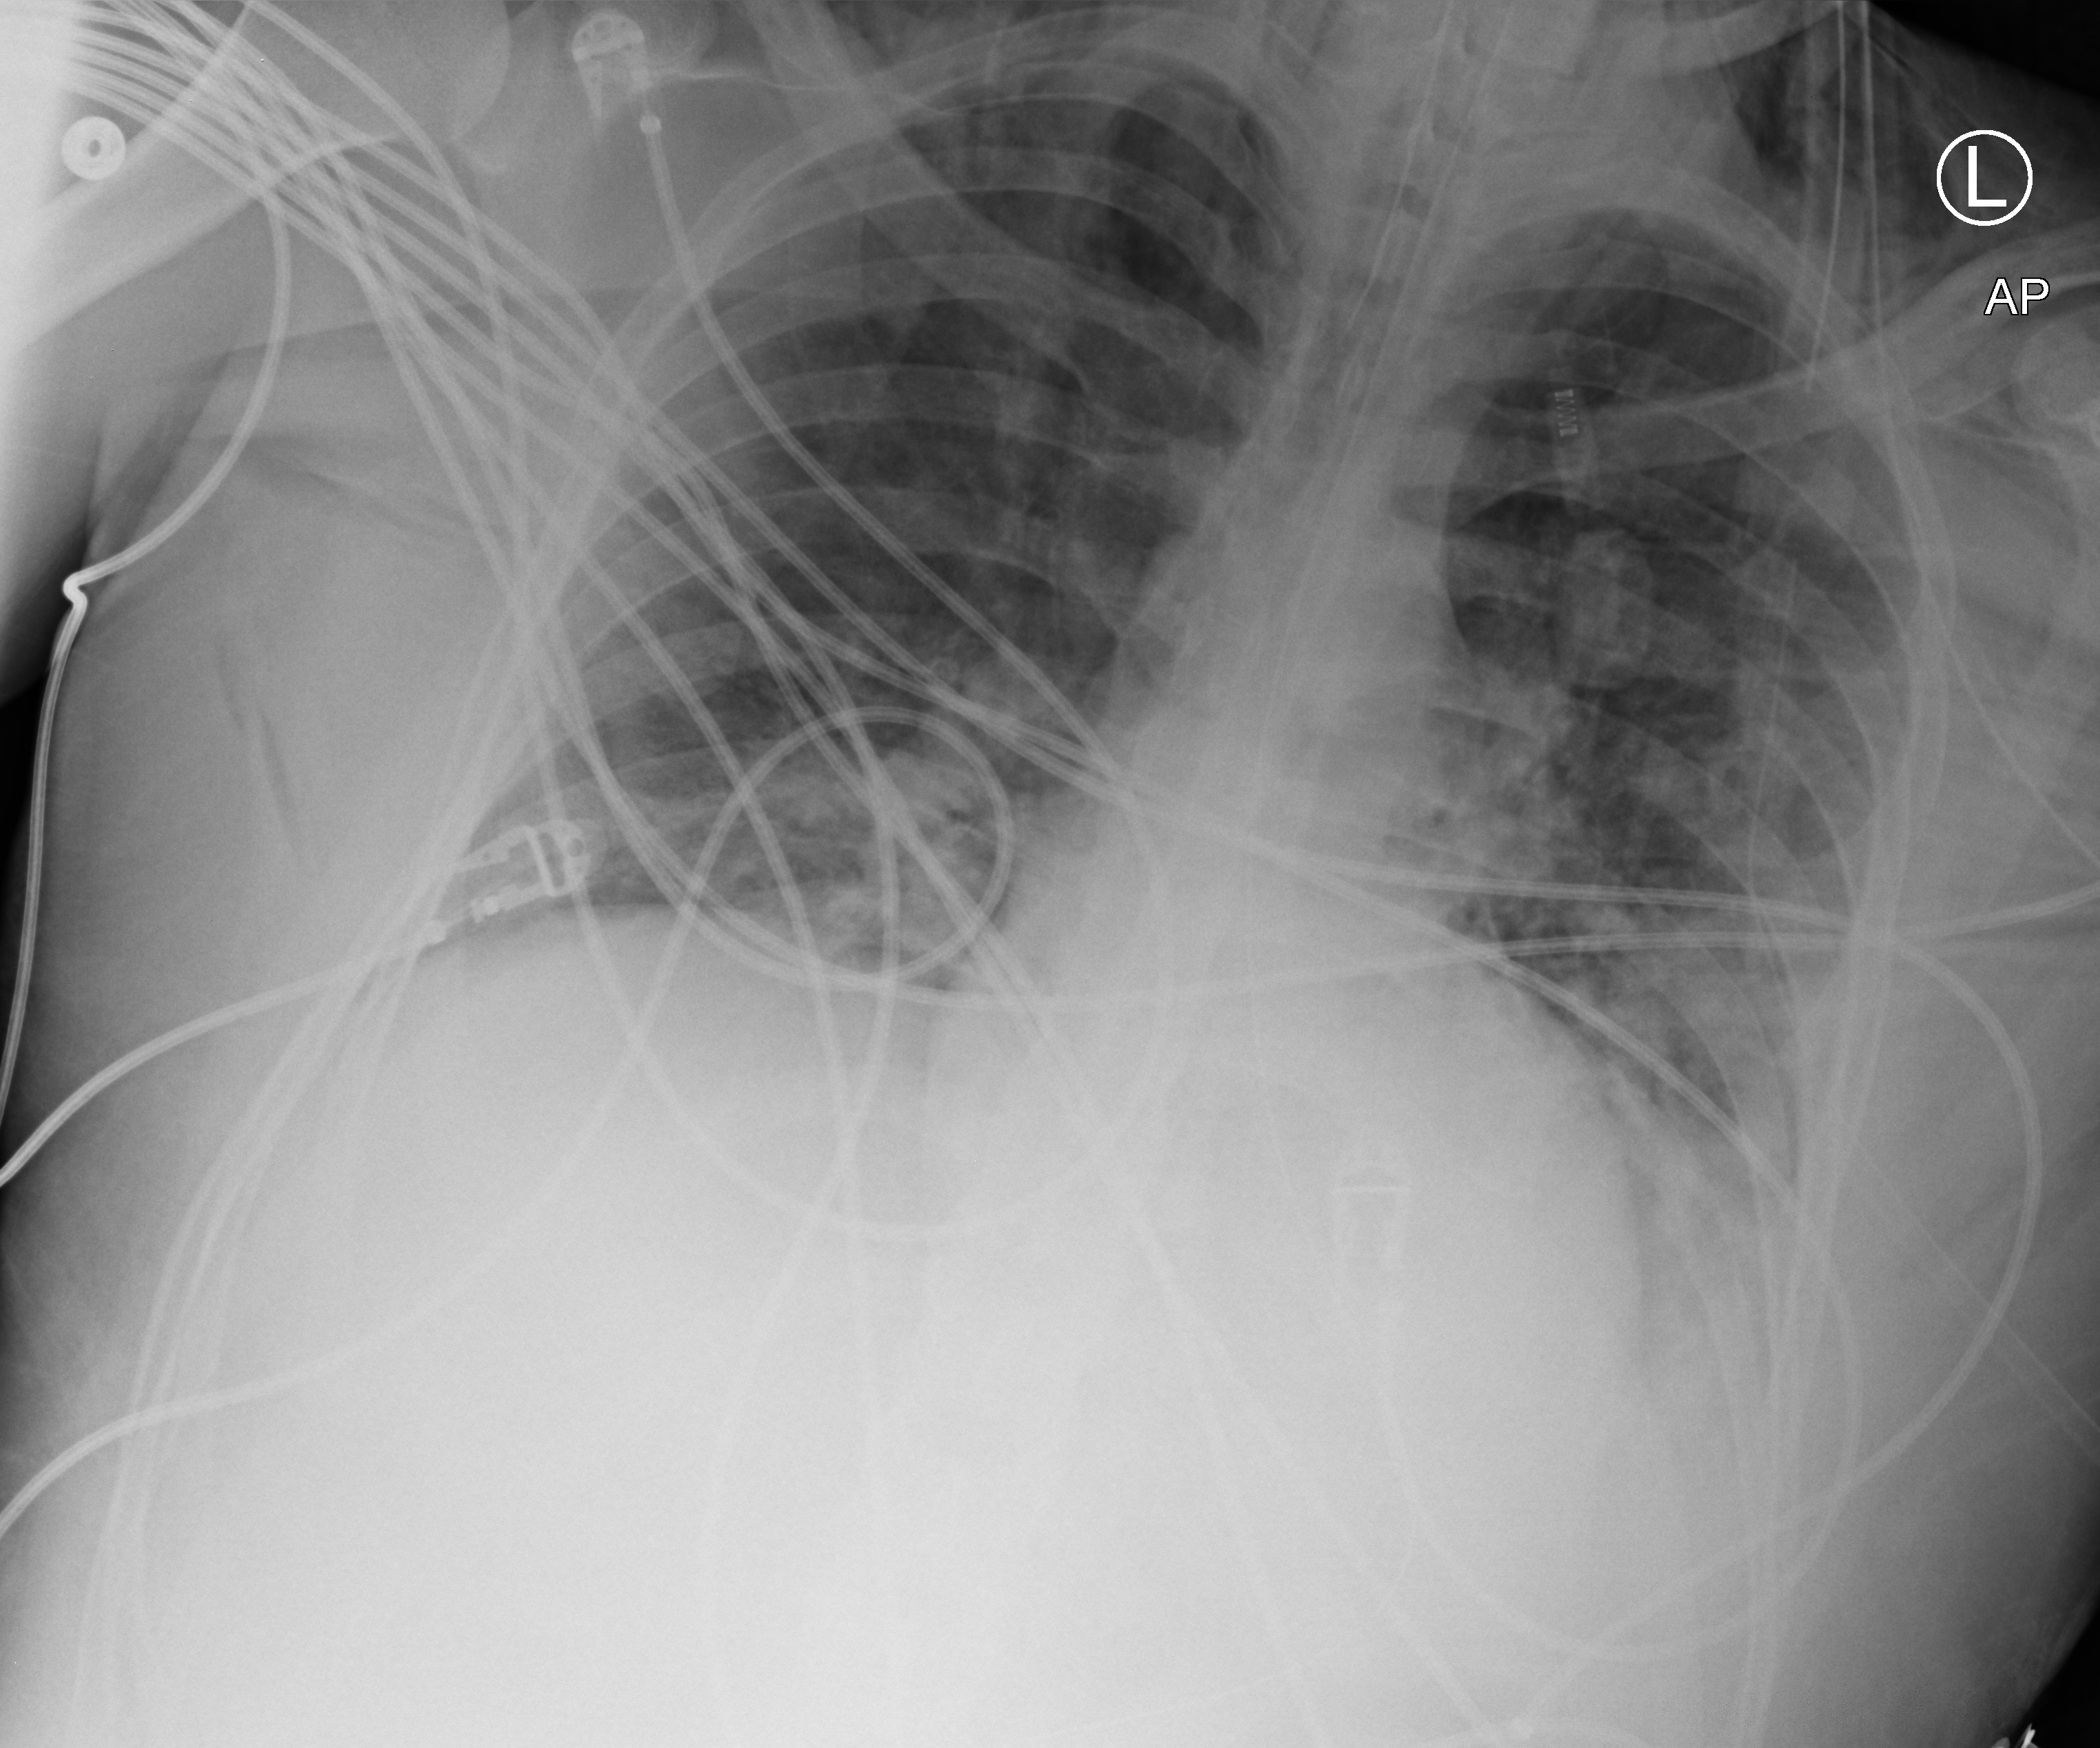
Bedside chest radiograph (computed radiography). Male patient hospitalised with COVID-19, age 18–59 years.
Admission-level facts for this patient (not findings on this image; timing relative to this image not recorded): mechanically ventilated during this hospital stay: yes; admitted to intensive care during this hospital stay: yes.